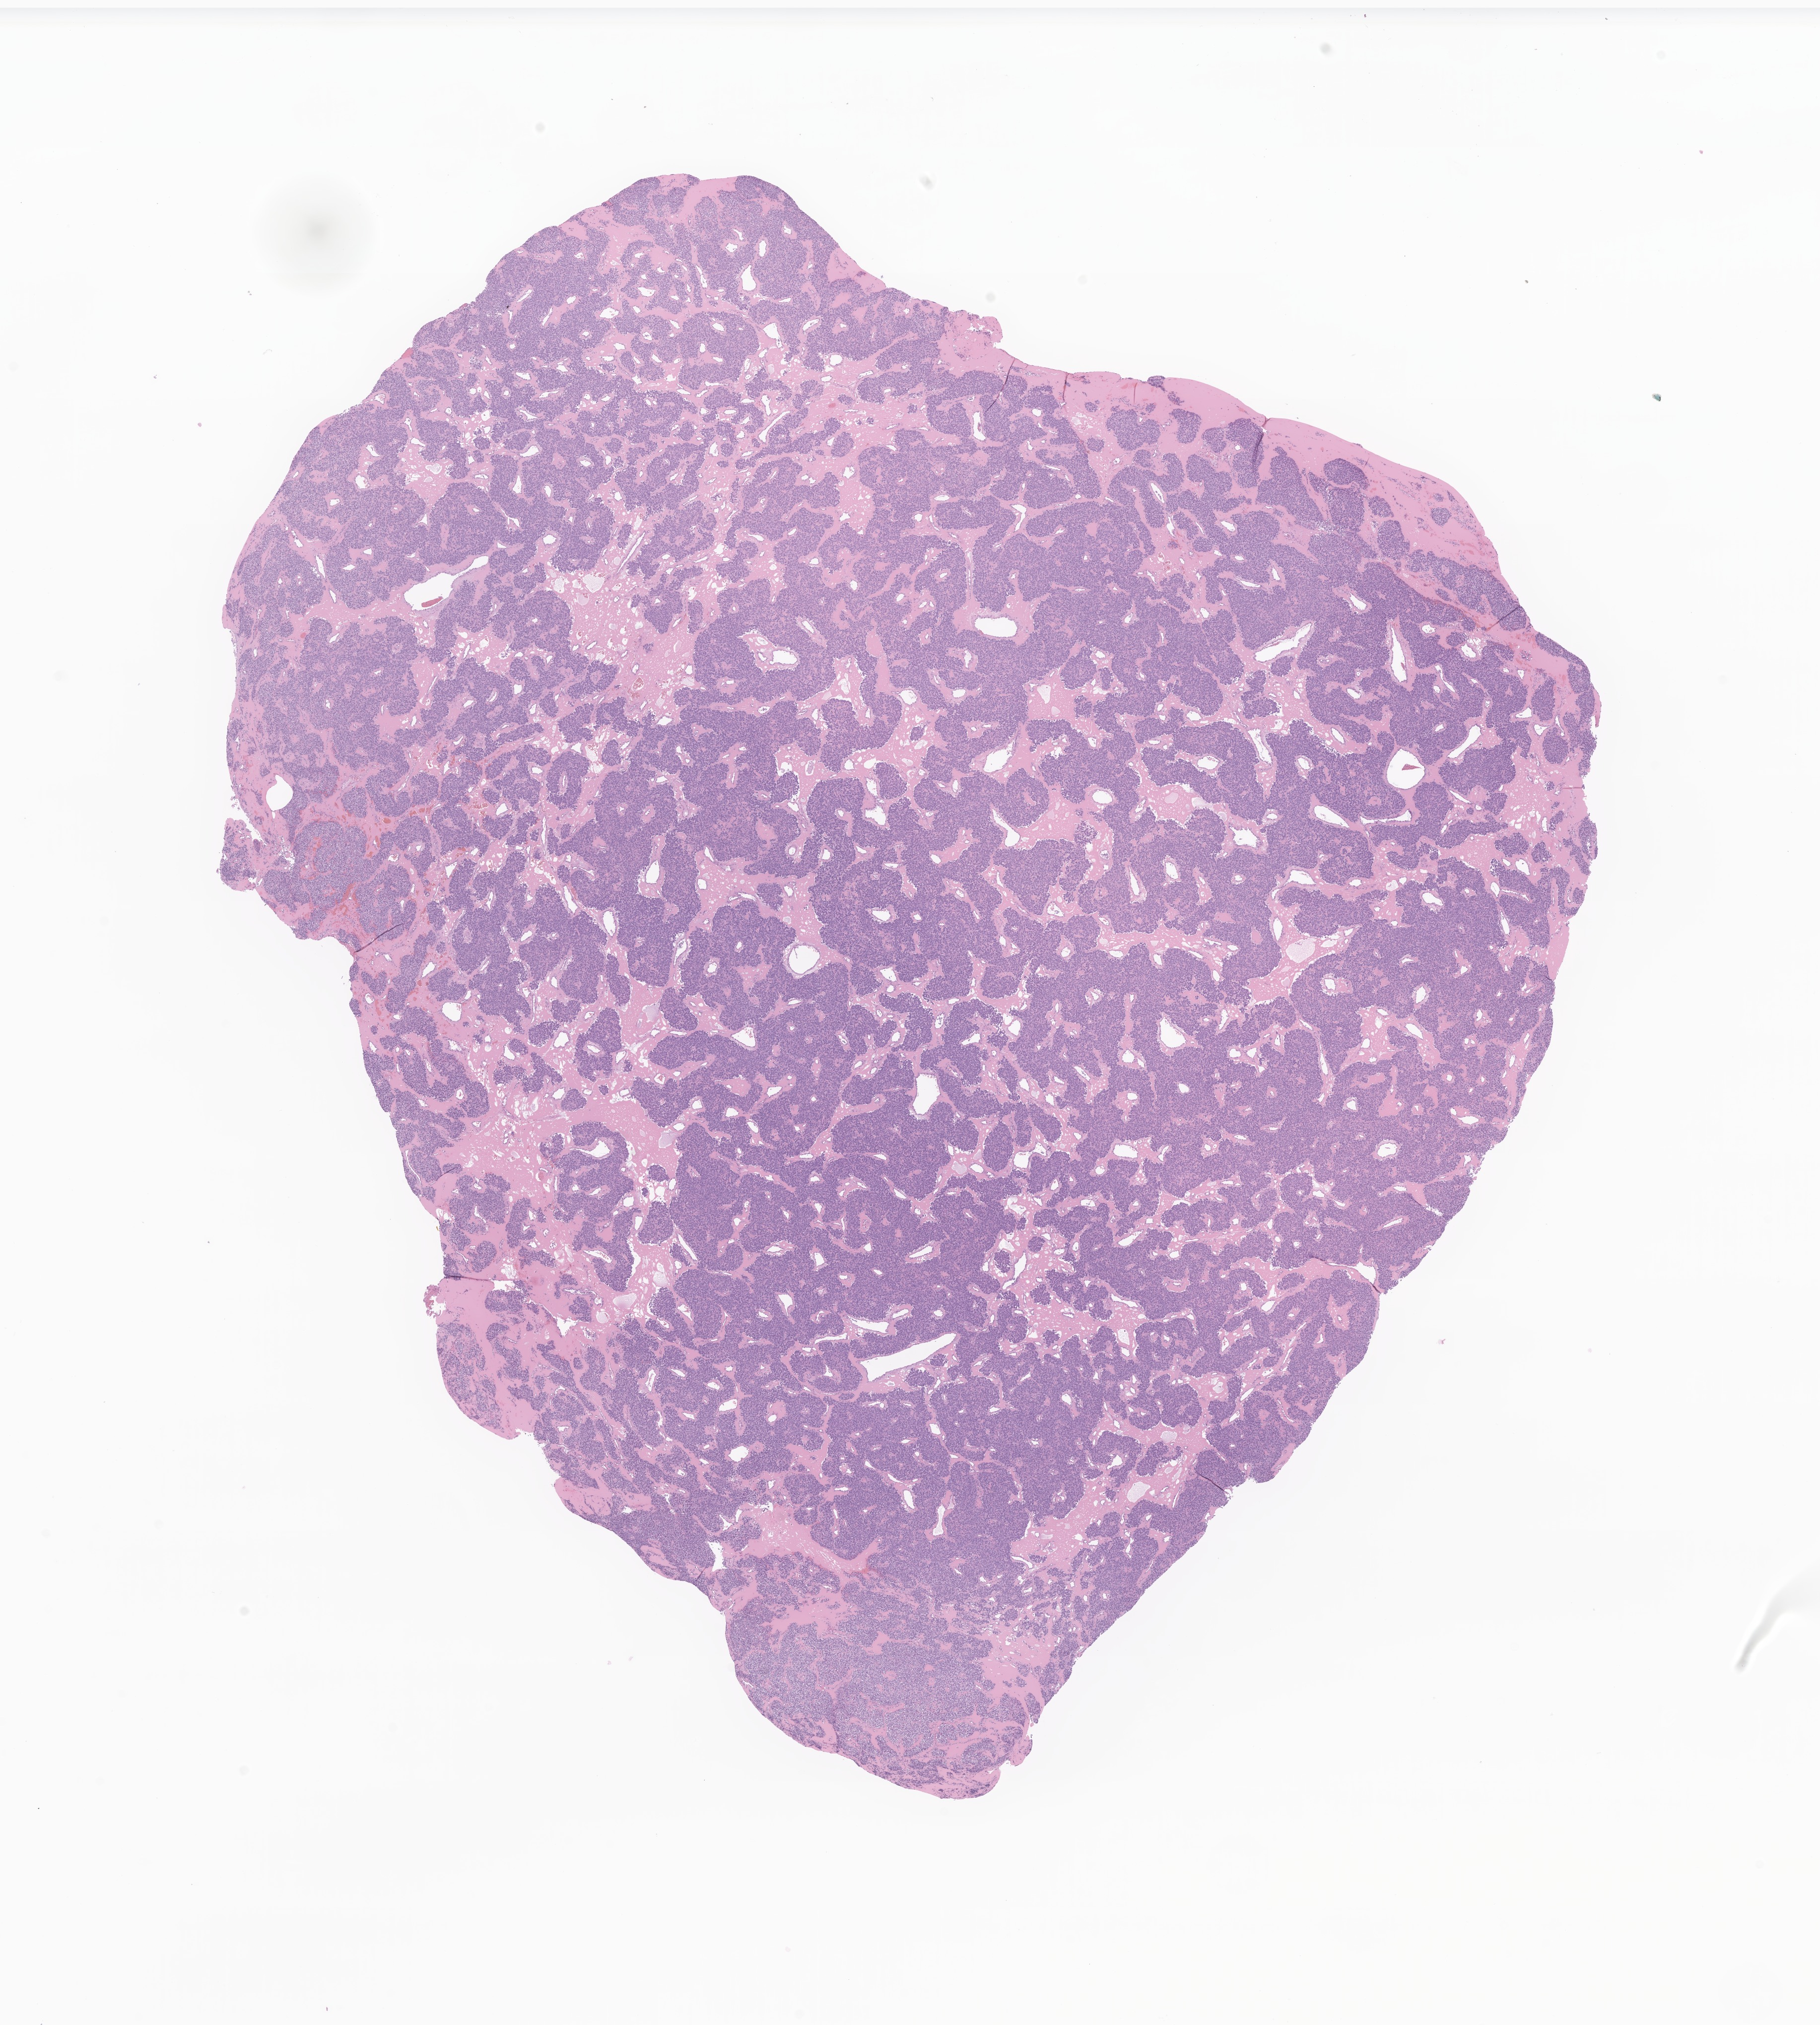
Digitized H&E-stained section of tumor tissue from the soft tissue of upper extremity, low-resolution overview of the scanned area, about 15.5 x 17.2 mm, FFPE section. Female patient, age 203 months (16 years 11 months).
Diagnosis: Ewing sarcoma. Tissue or organ of origin (case record): connective, subcutaneous and other soft tissues of upper limb and shoulder.